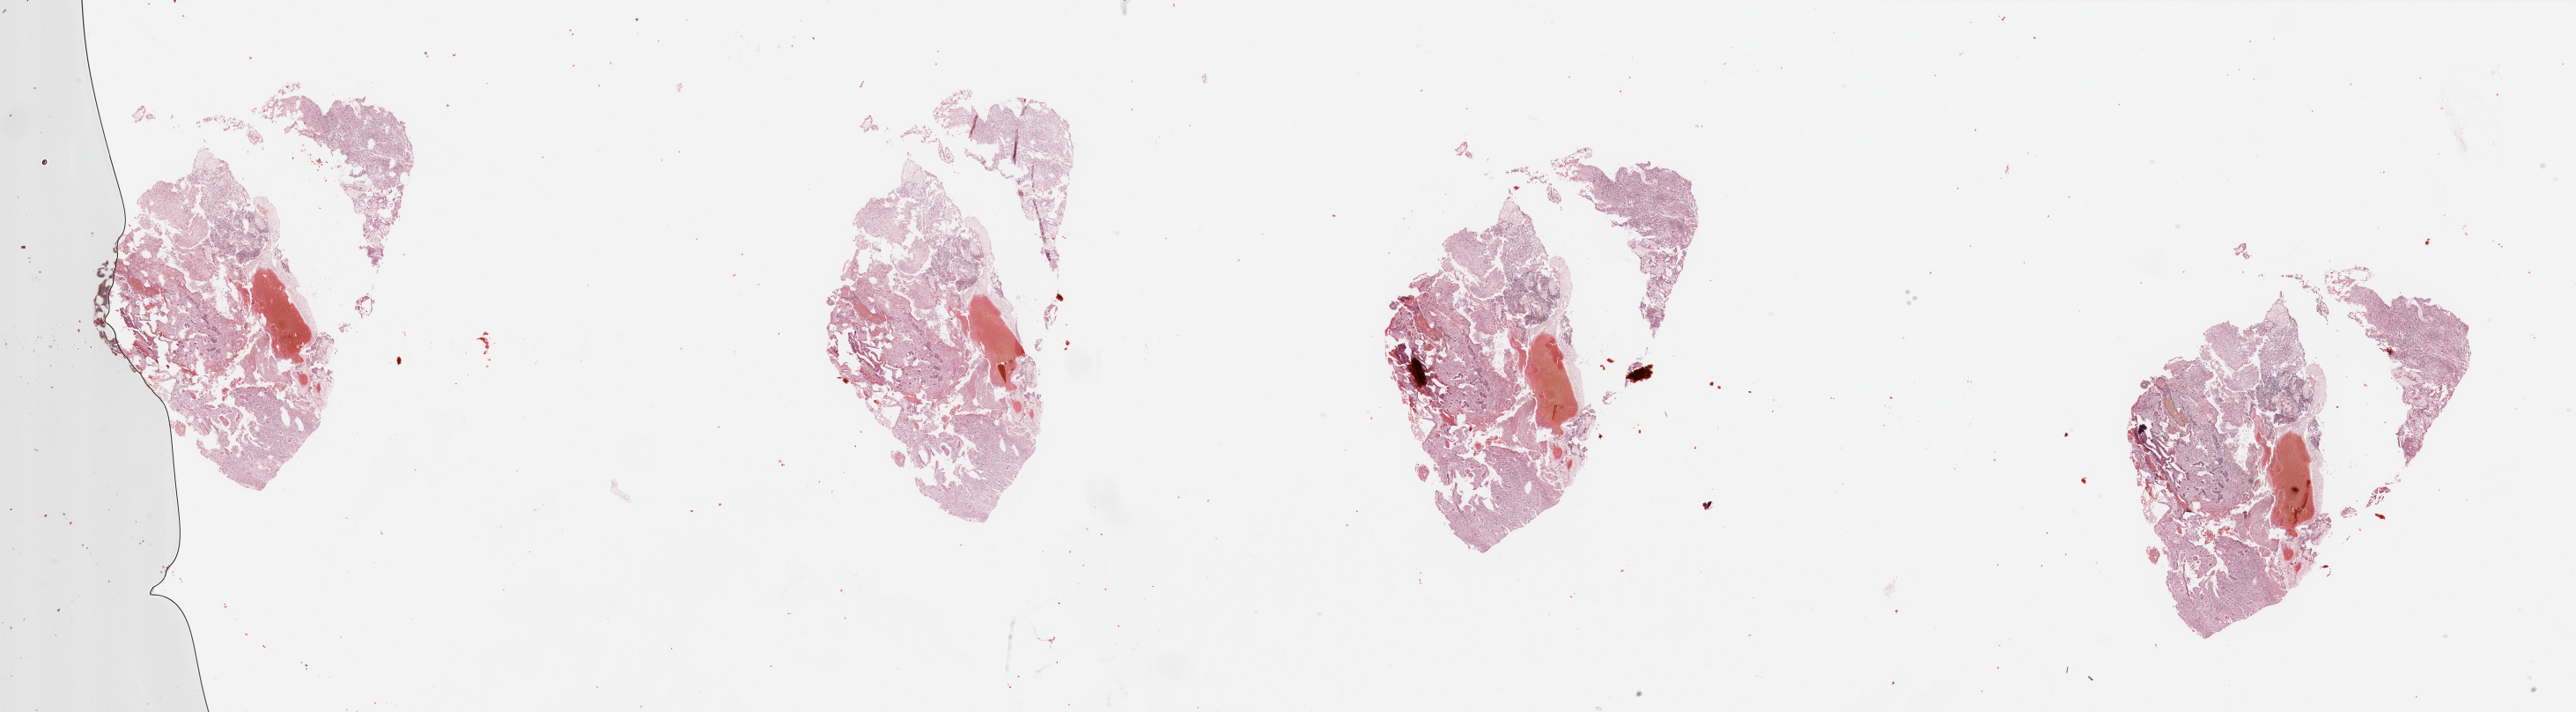
Digitized Hematoxylin and eosin (H&E) stained tissue section (whole slide) — whole scanned area (about 46.3 x 12.8 mm, slide scanned at 20x) shown as a low-resolution overview; brain, tumour tissue. 40-year-old male patient.
- diagnosis: Glioblastoma
- primary tumour site (as recorded): frontal lobe